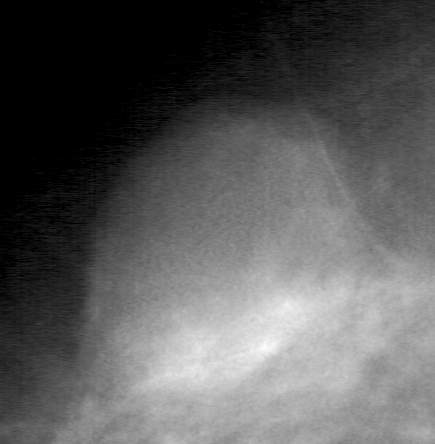
Region of interest cut from a scanned film mammogram (one marked finding), left breast, CC view.
- Finding: mass, shape lobulated, margins circumscribed; BI-RADS assessment category 4; pathology result (as recorded, not read from the image): benign.